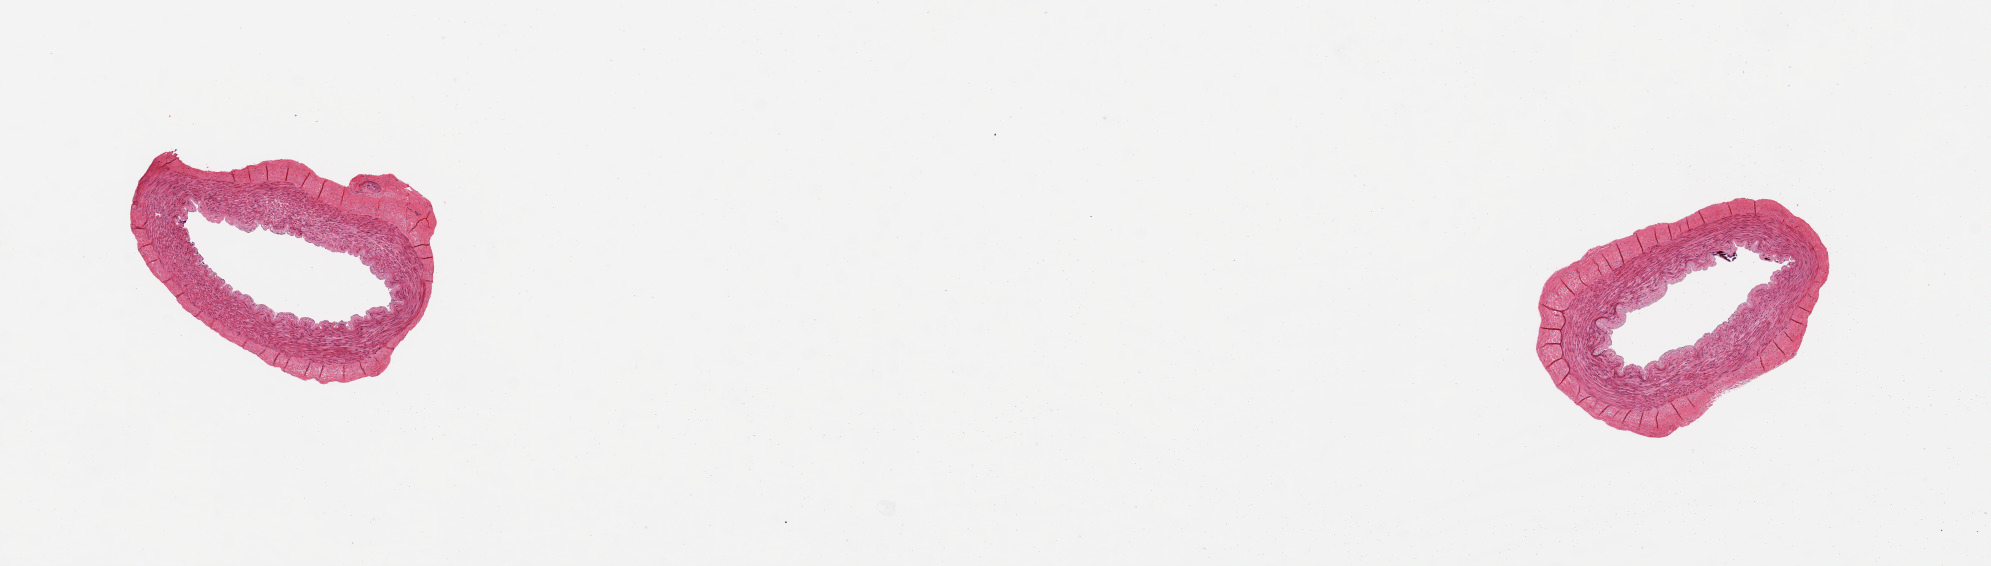
Digitized H&E-stained section, brightfield — shown as a low-resolution overview of the whole scanned area (about 15.8 x 4.5 mm), PAXgene-fixed, paraffin-embedded tissue, section of tibial artery (target tissue), tissue donor sample. Donor: male.
- pathologist's review note for this sample: 2 pieces, small intimal calcifications; no plaques